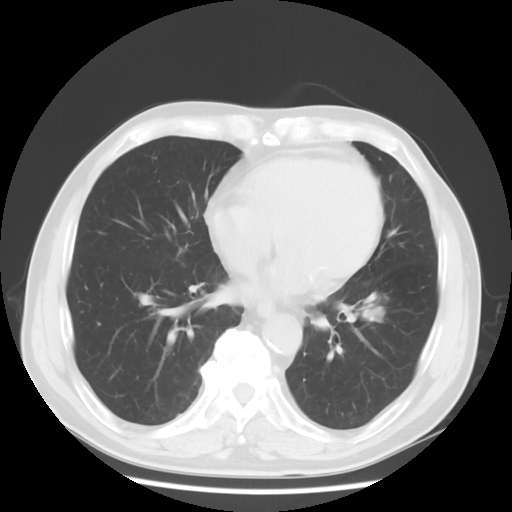
Chest CT, one axial slice; slice 26 of 68 in the series (ordered by position); 120 kVp; lung window (W 1500 / L -600 HU); 5 mm slice thickness; 512 × 512 image matrix. Patient: male, 71 years. Case-level facts recorded for this patient, not image findings: clinical TNM (as recorded): T1c N1 M0; histopathological grade: G2-3.
Annotated regions visible in this slice (bounding box drawn by a radiologist):
- lung tumour (recorded histology: adenocarcinoma): bounding box (x1, y1, x2, y2) in pixels: (356, 288, 395, 333)